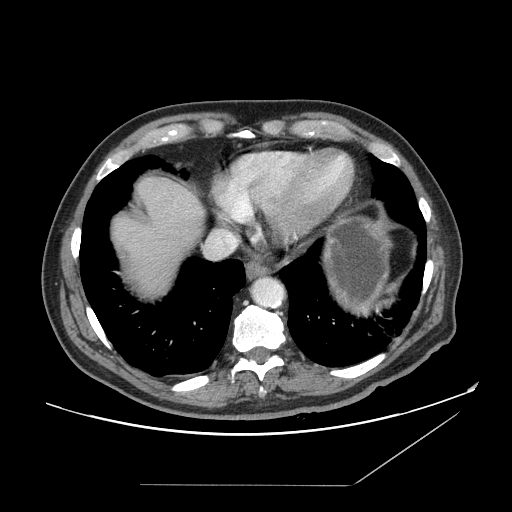
Contrast-enhanced abdominal CT, one axial slice. Slice 140 of 166 in the series (ordered by position). Intravenous contrast given. Soft-tissue window (W 400 / L 40 HU). 2.5 mm slice thickness. 512 × 512 image matrix, field of view 416 × 416 mm. Male patient, age 80 years. Case-level facts recorded for this patient, not image findings: diagnosis: colorectal cancer liver metastases, imaged before liver resection; multiple liver metastases: no; largest metastasis: 2.2 cm; disease in both lobes: no.
Annotated regions visible in this slice (manually delineated by an expert):
- liver: box from (x=110, y=177) to (x=206, y=299) px
- planned liver remnant (the part of the liver to remain after resection): (x=109, y=177)–(x=206, y=257)